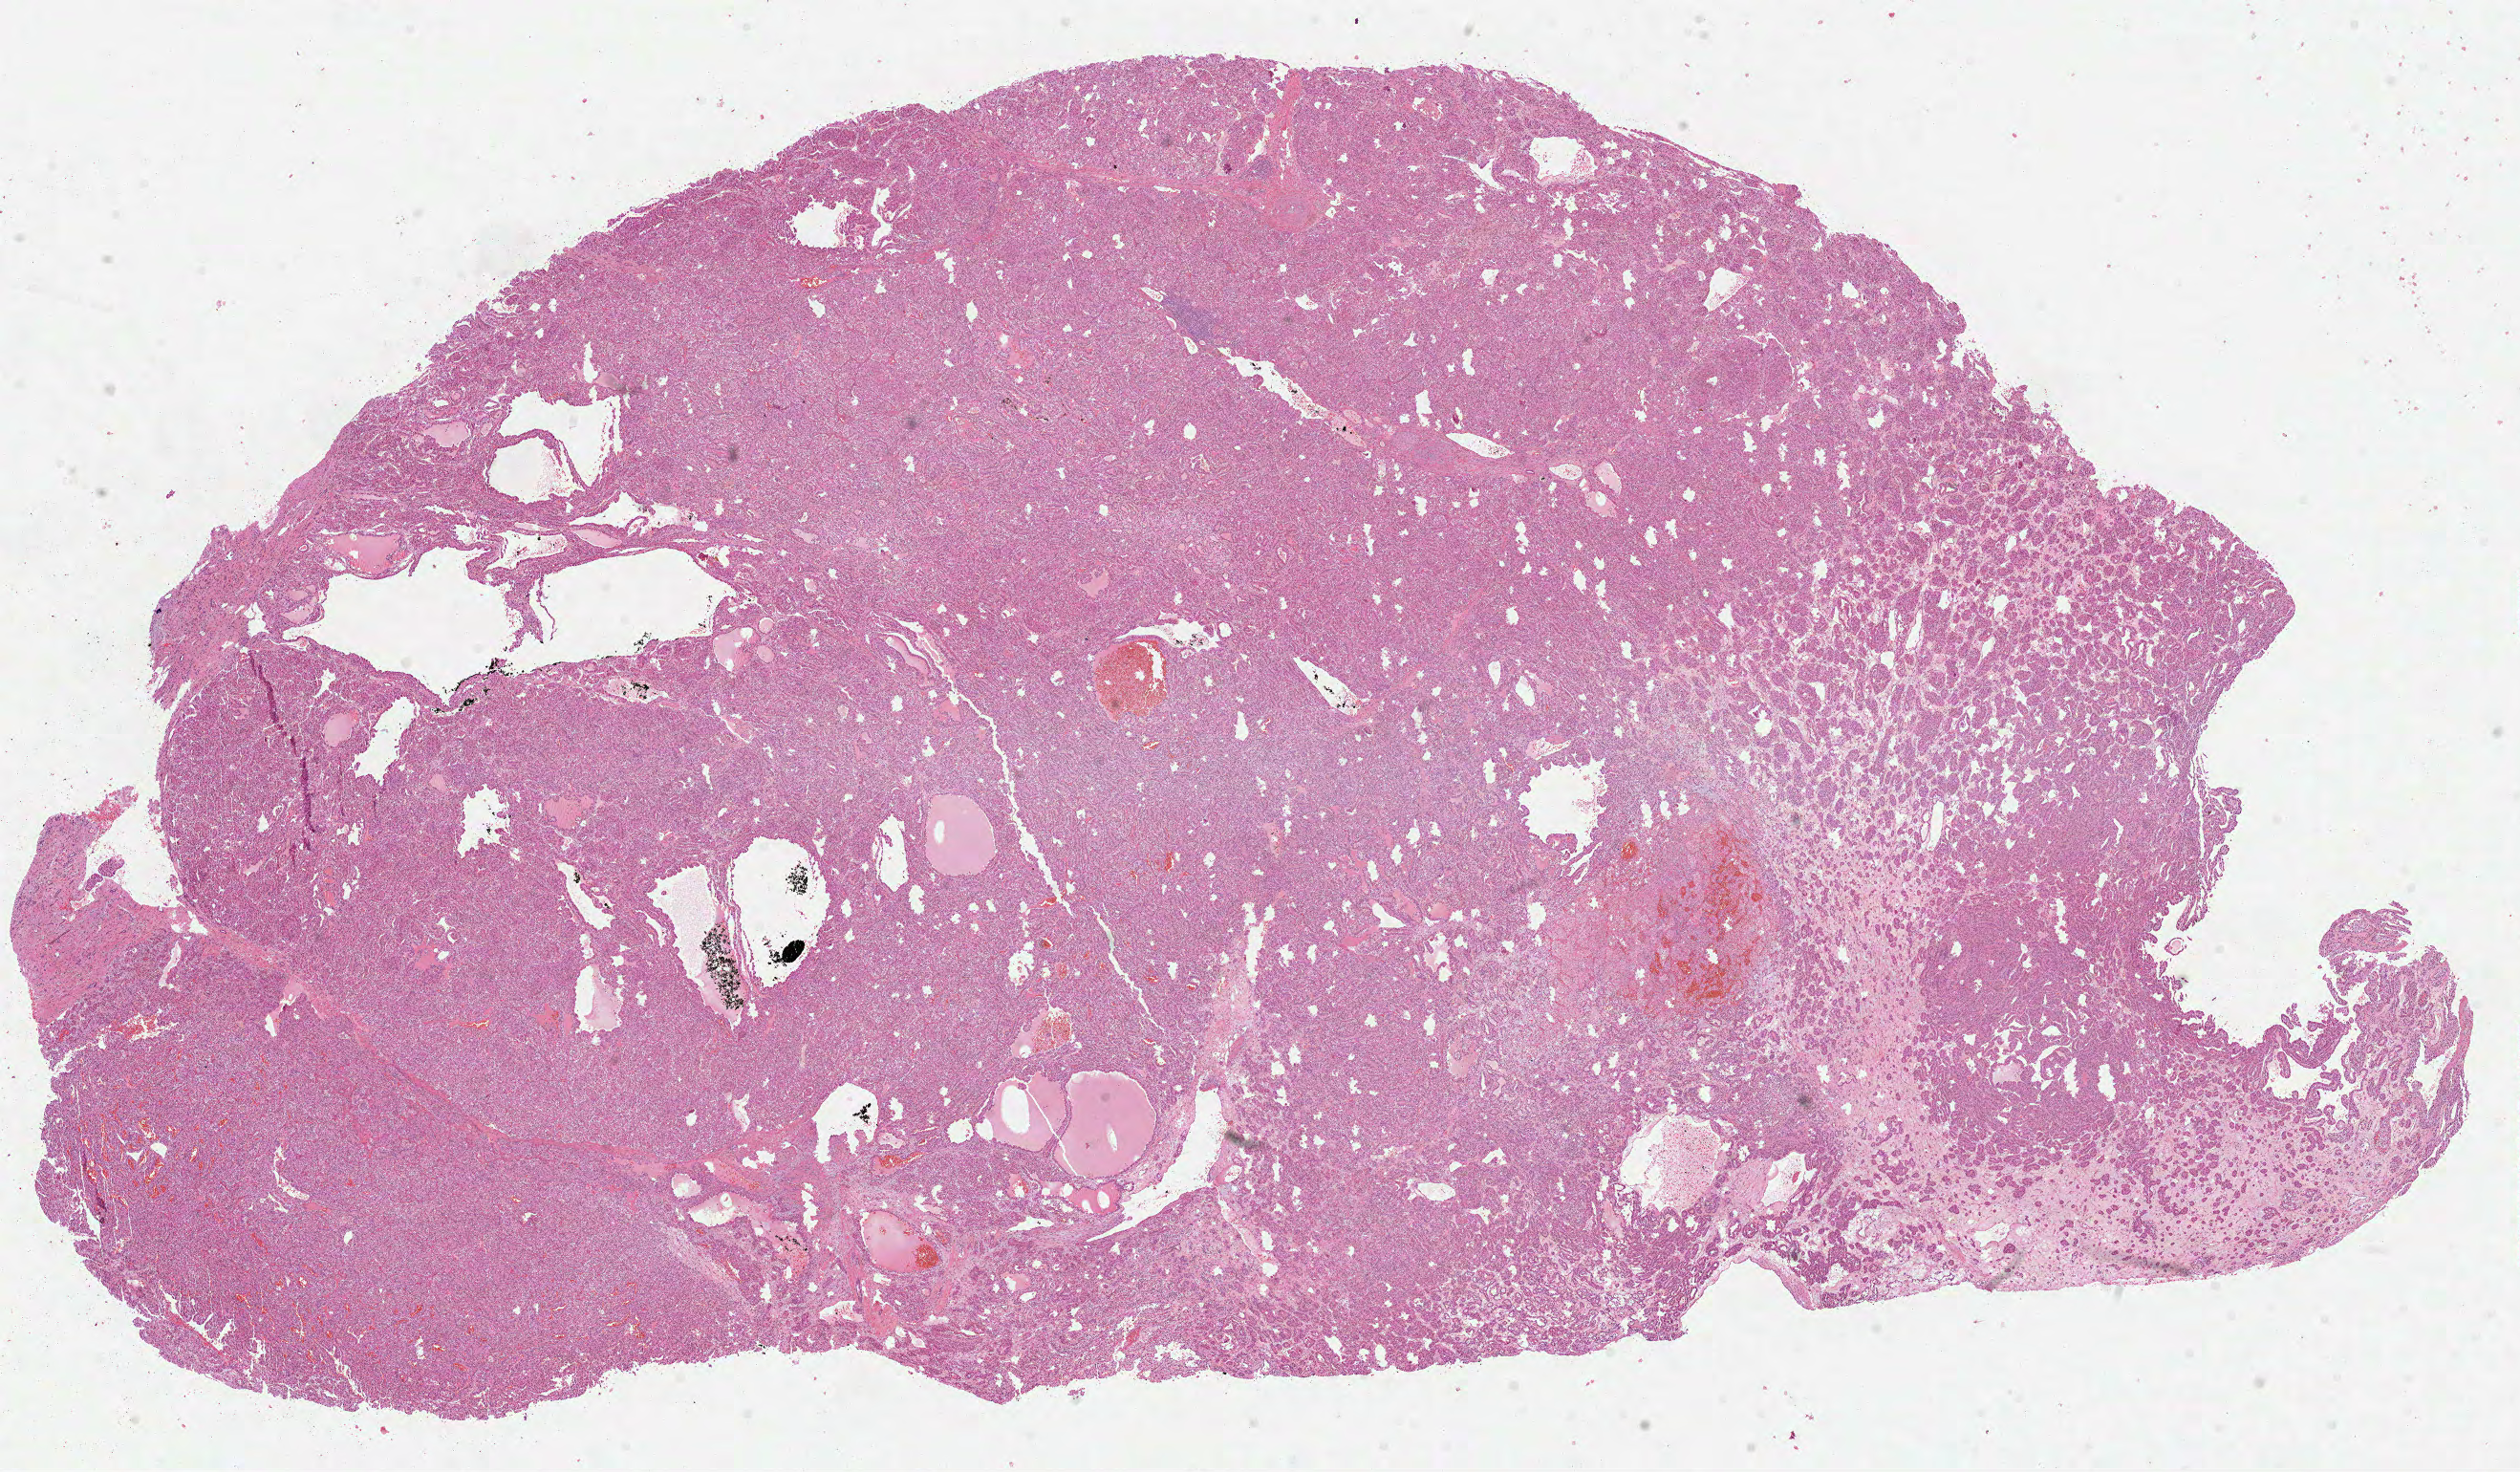
Digitized Hematoxylin and eosin (H&E) stained tissue section (whole slide) — a low-resolution overview of the entire scanned area, about 21.3 x 12.4 mm (acquisition: 40x scan), FFPE section, kidney, primary tumour sample. Male, age 59 years at initial diagnosis. Histologic grade: G3 (poorly differentiated).
* histologic diagnosis: Clear cell adenocarcinoma, NOS
* AJCC pathologic stage: I
* laterality: right